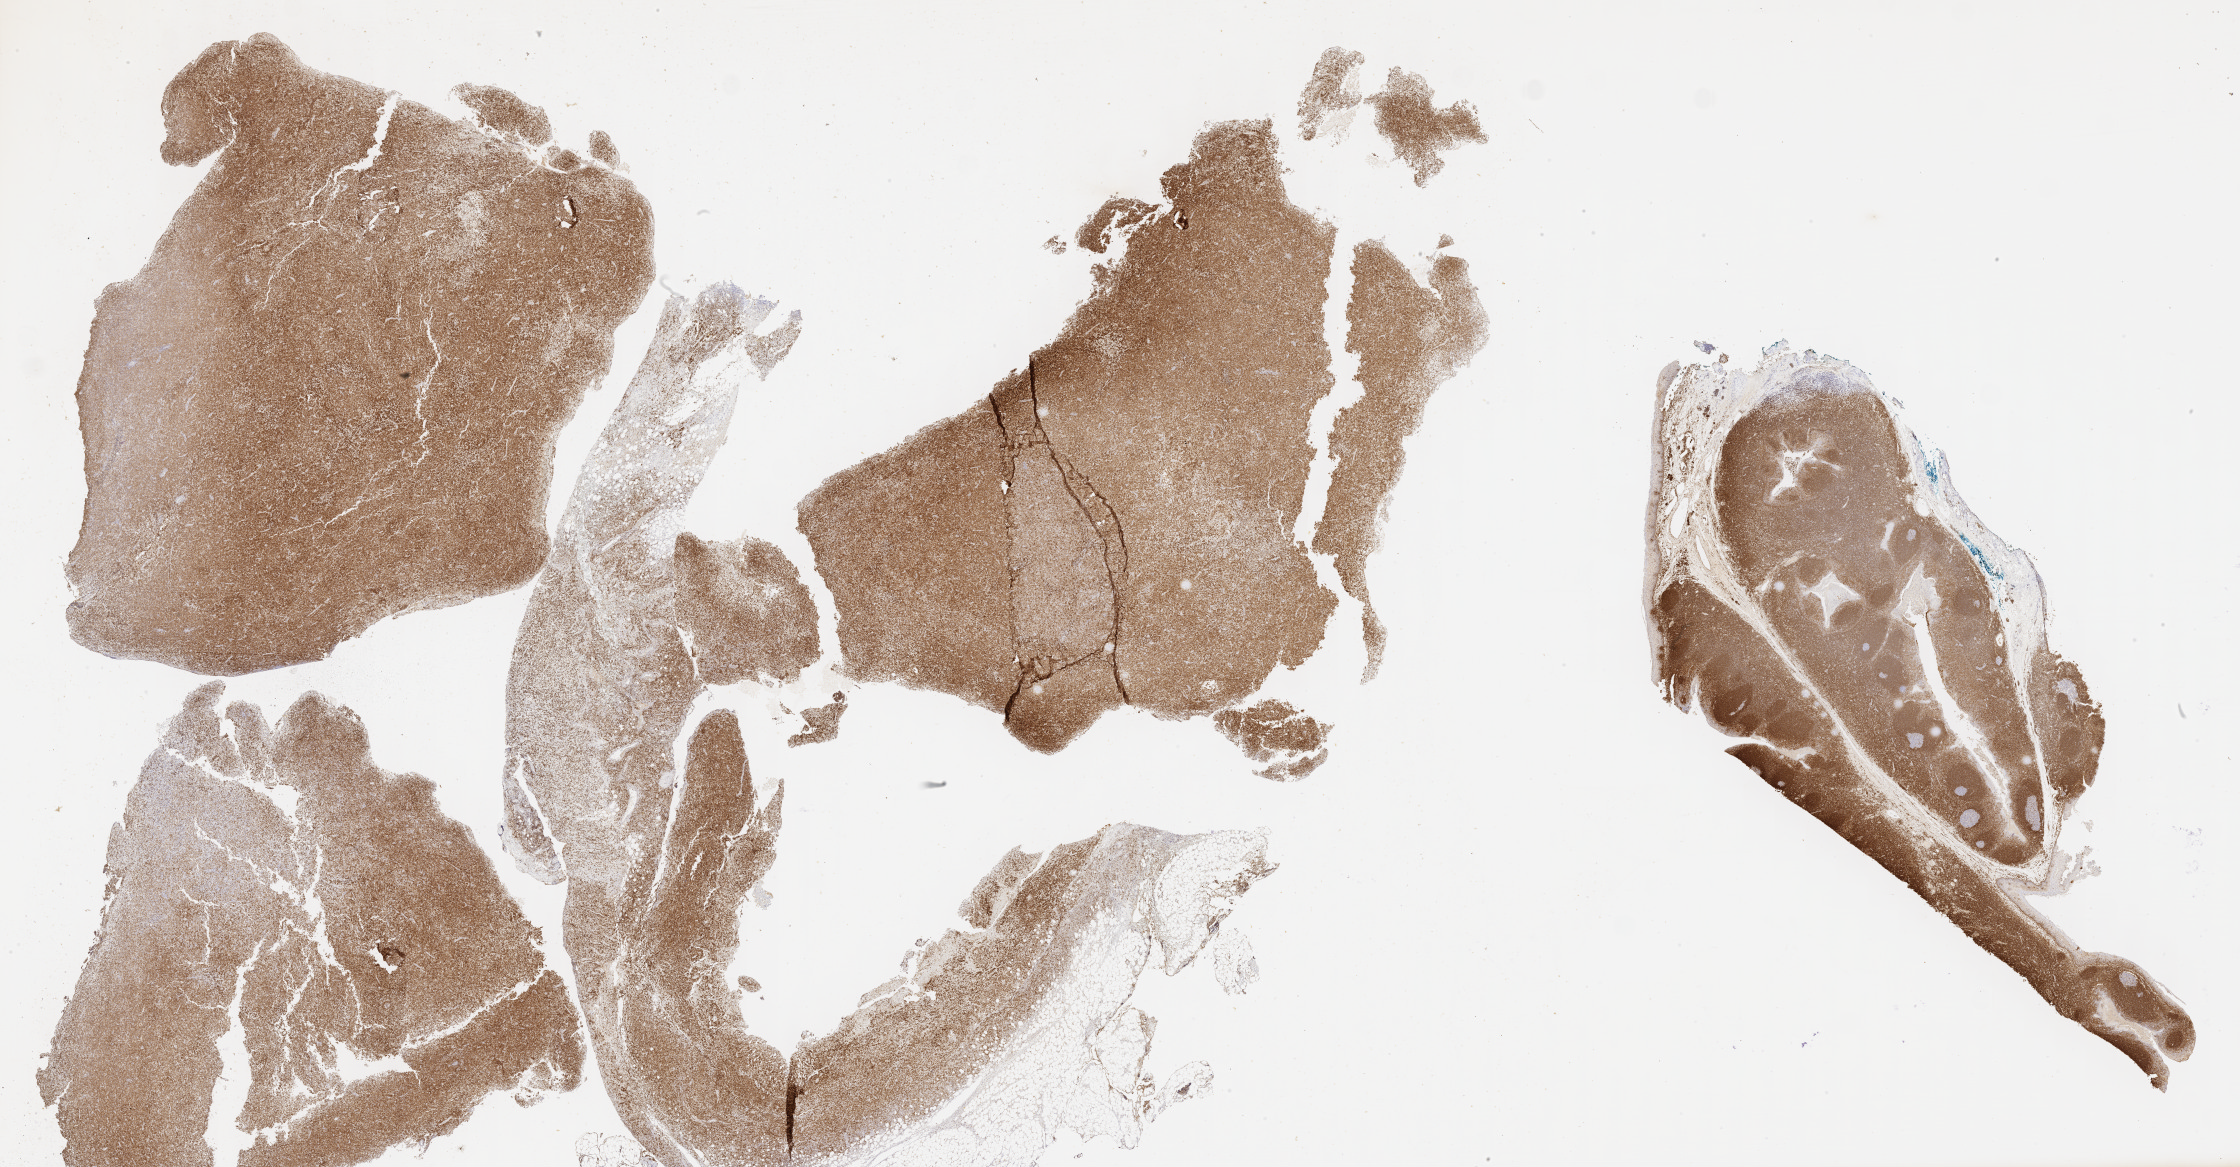
Immunohistochemistry (IHC) whole-slide image stained for BCL2 — shown as a low-resolution overview of the whole scanned area (about 36.2 x 18.9 mm). Patient sex: female.
- specimen: tumor tissue